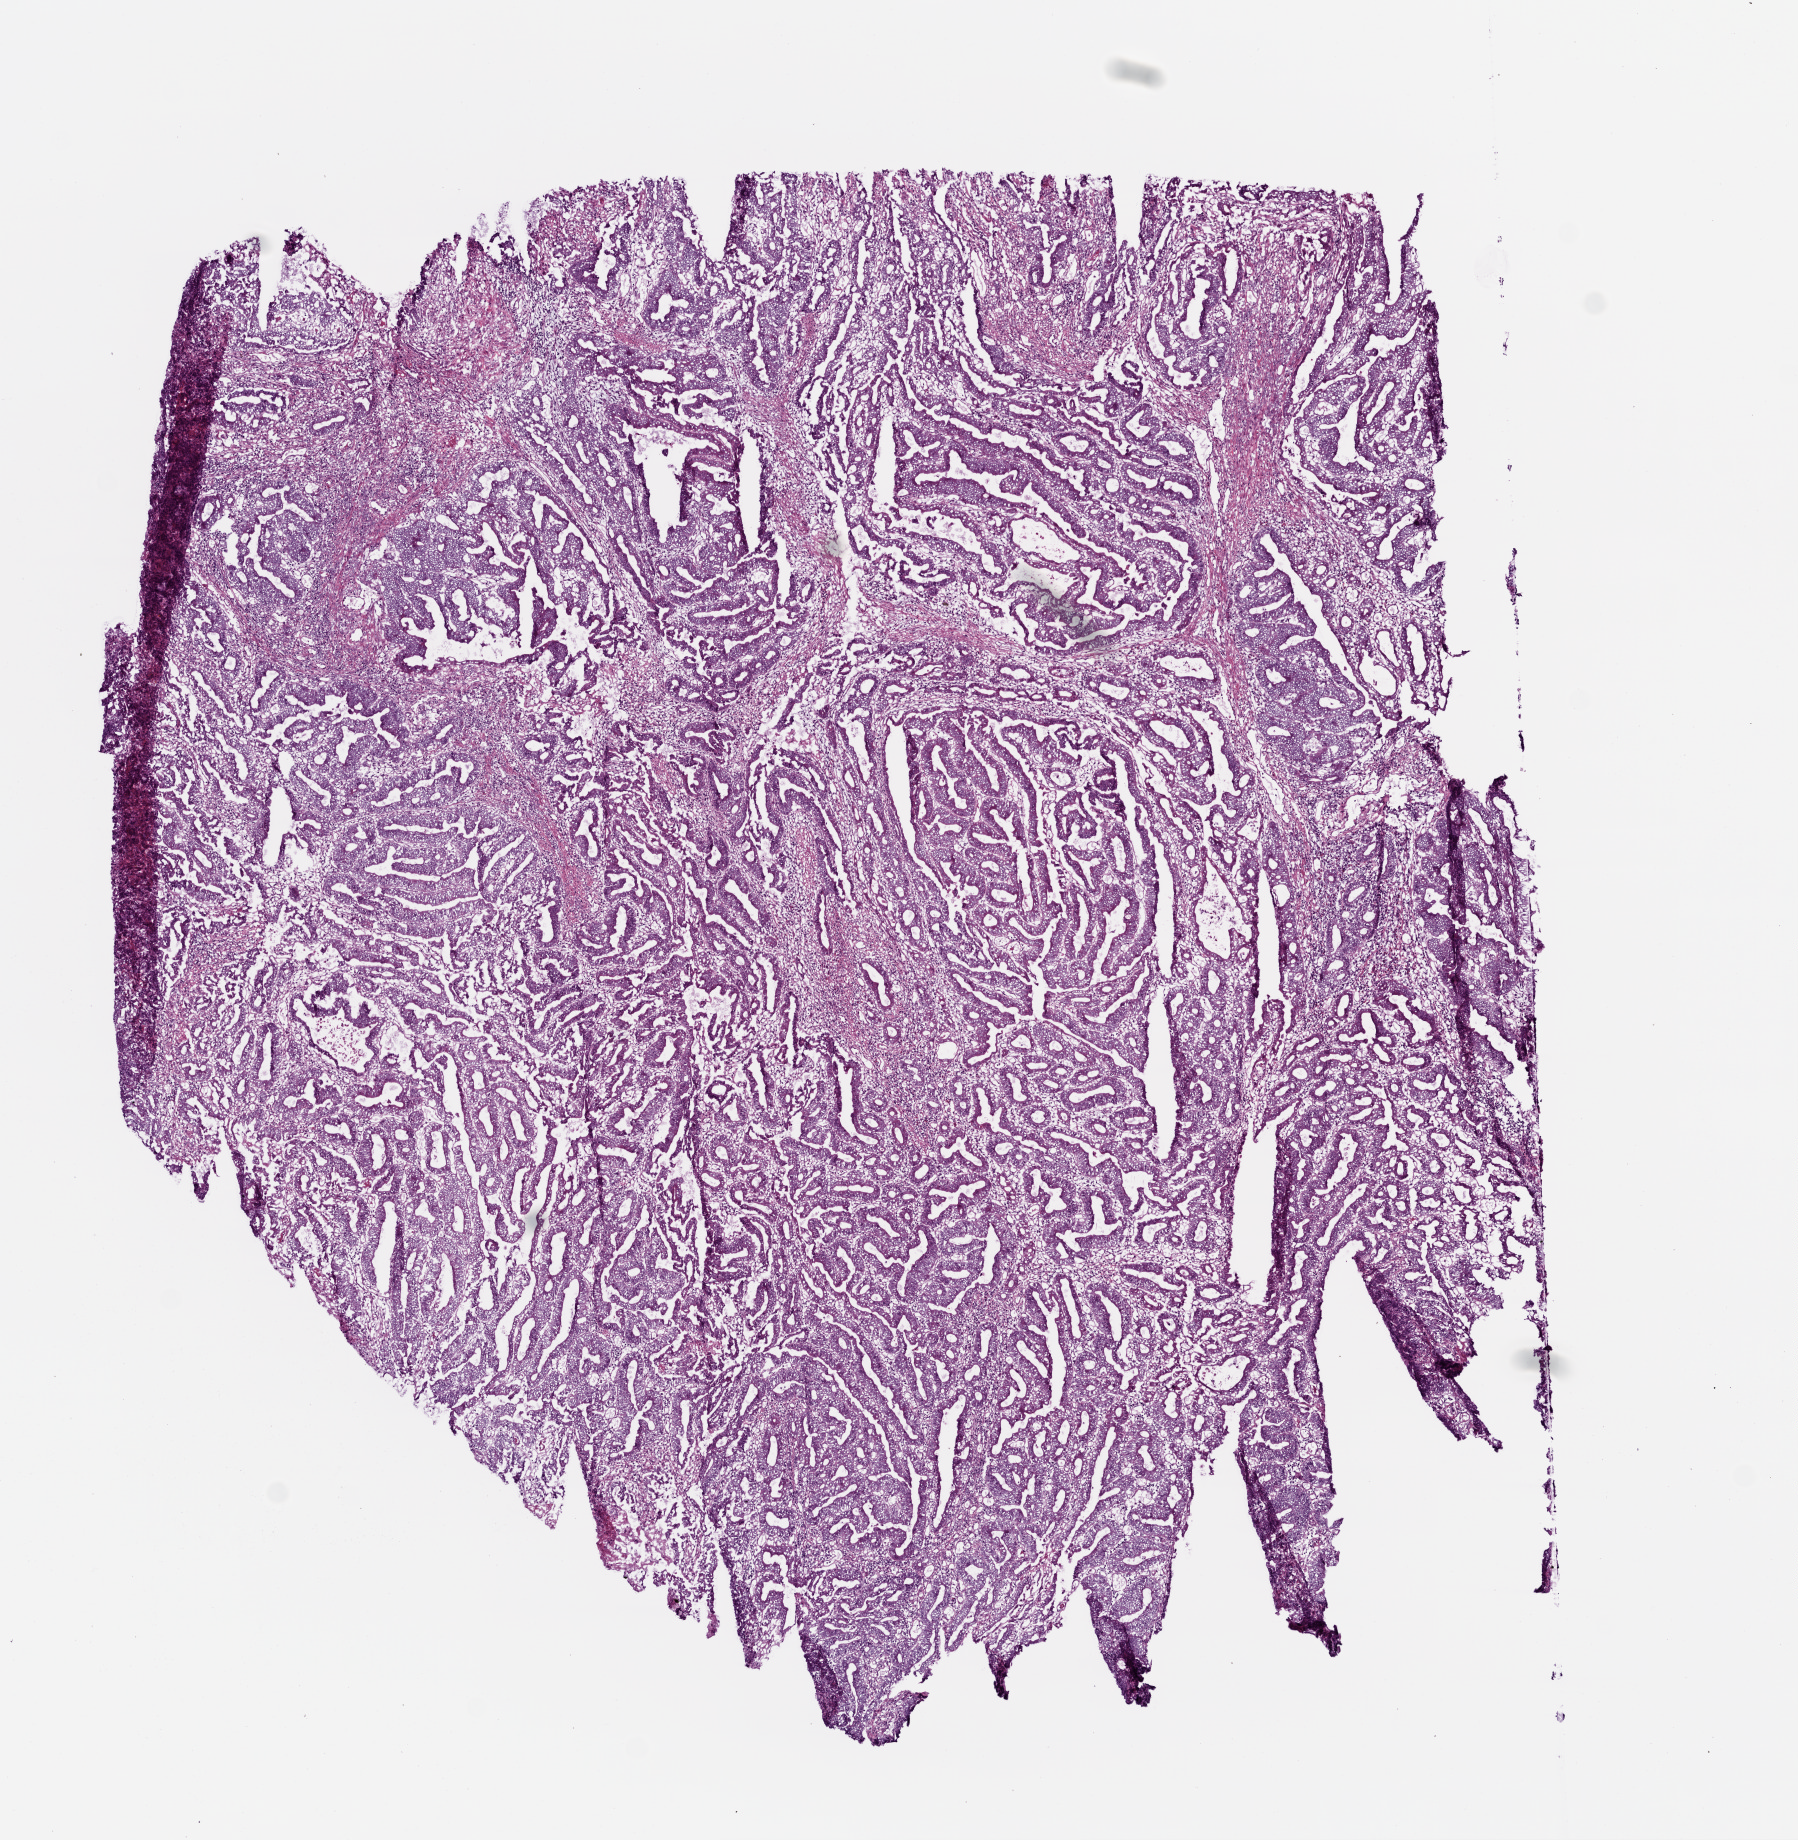
H&E whole-slide image — low-resolution overview of the scanned area, about 7.3 x 7.4 mm. Frozen section from the top of the tissue portion. Rectum, primary tumour sample. Female, age 73 years at initial diagnosis. Slide review estimates, as recorded: tumour cells 85%, tumour nuclei 80%, normal cells 0%, stromal cells 15%, necrosis 0%.
- AJCC pathologic stage: I
- lymph nodes positive (case pathology): 0 of 24 examined
- pathologic diagnosis: Adenocarcinoma, NOS (rectosigmoid junction)